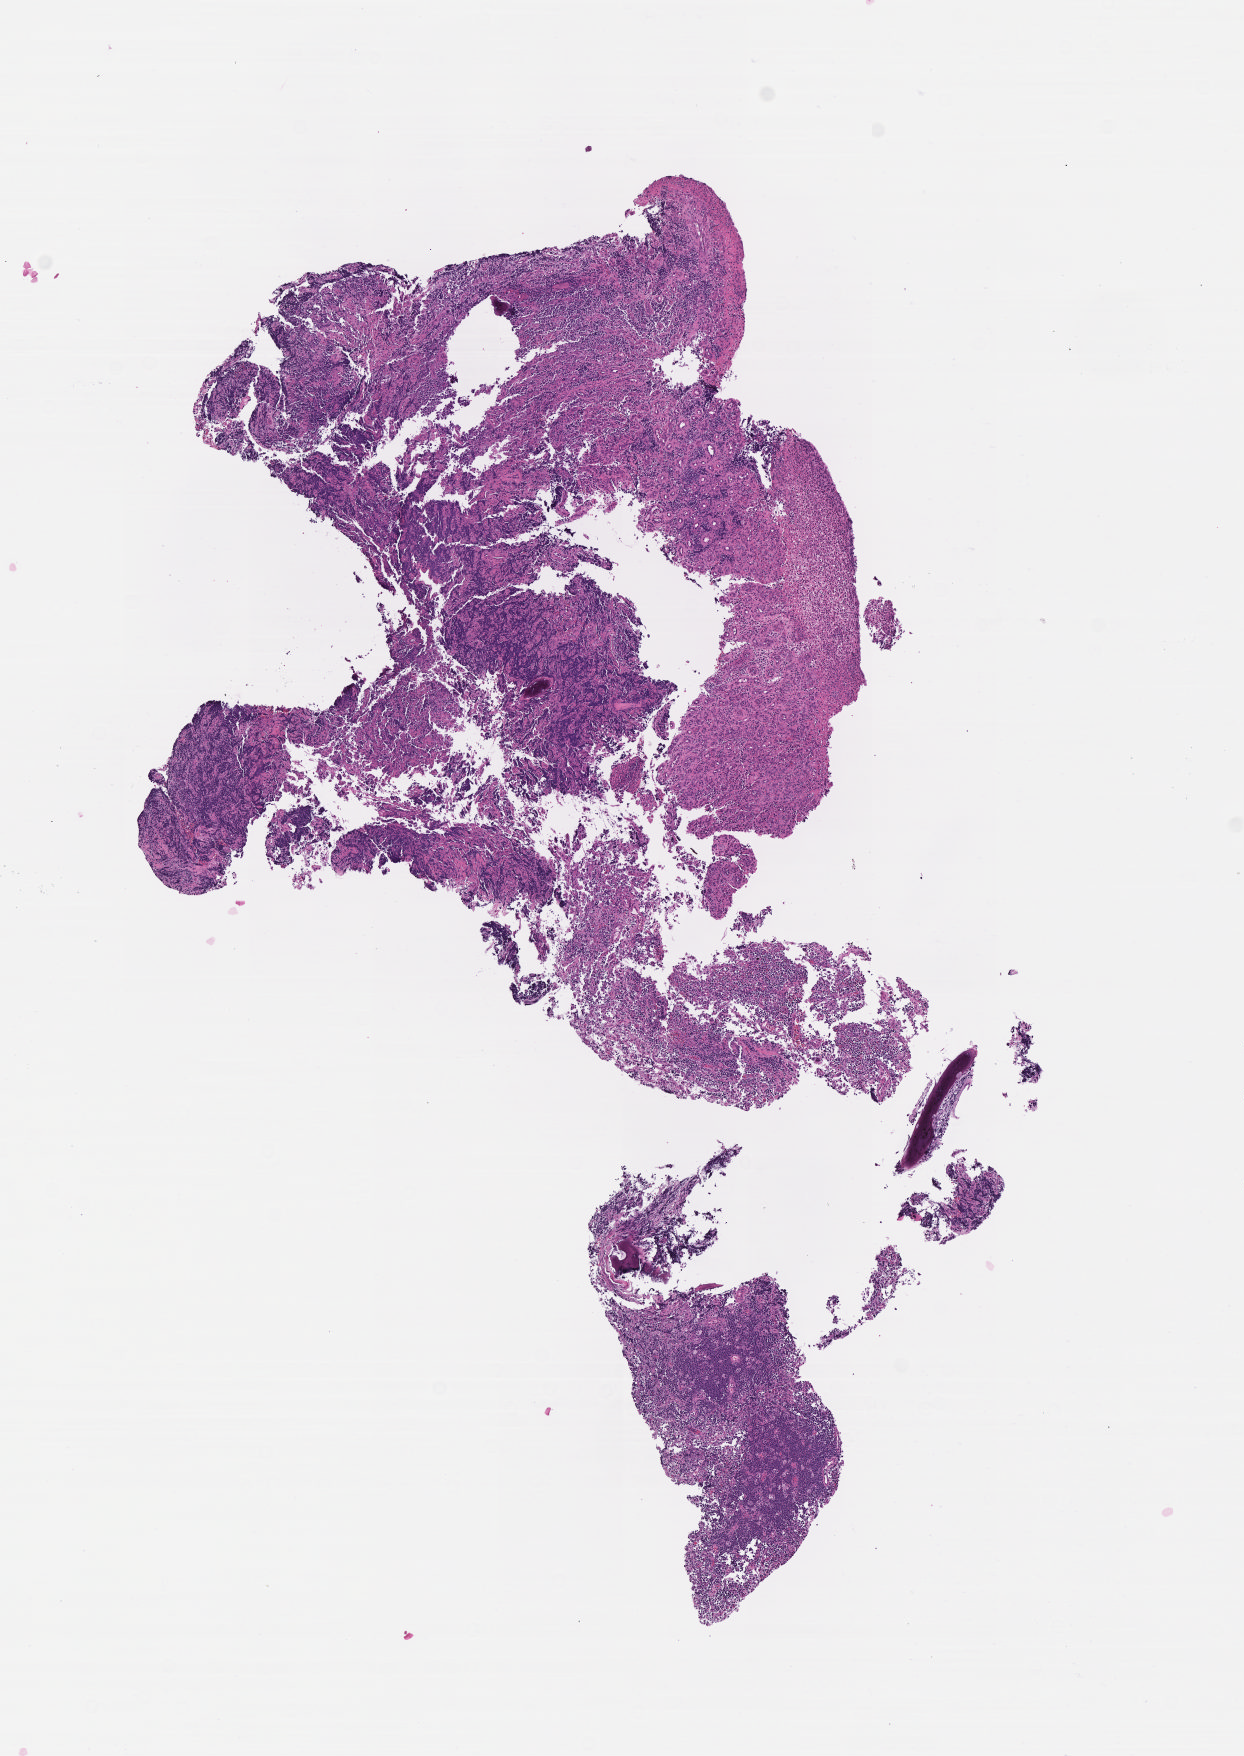
Digitized hematoxylin and eosin (H&E)-stained section — whole scanned area (about 5.0 x 7.1 mm) shown as a low-resolution overview, tumor tissue, anatomic site: gum of mandible. Patient male; aged 10.
- histologic diagnosis: Burkitt lymphoma, NOS